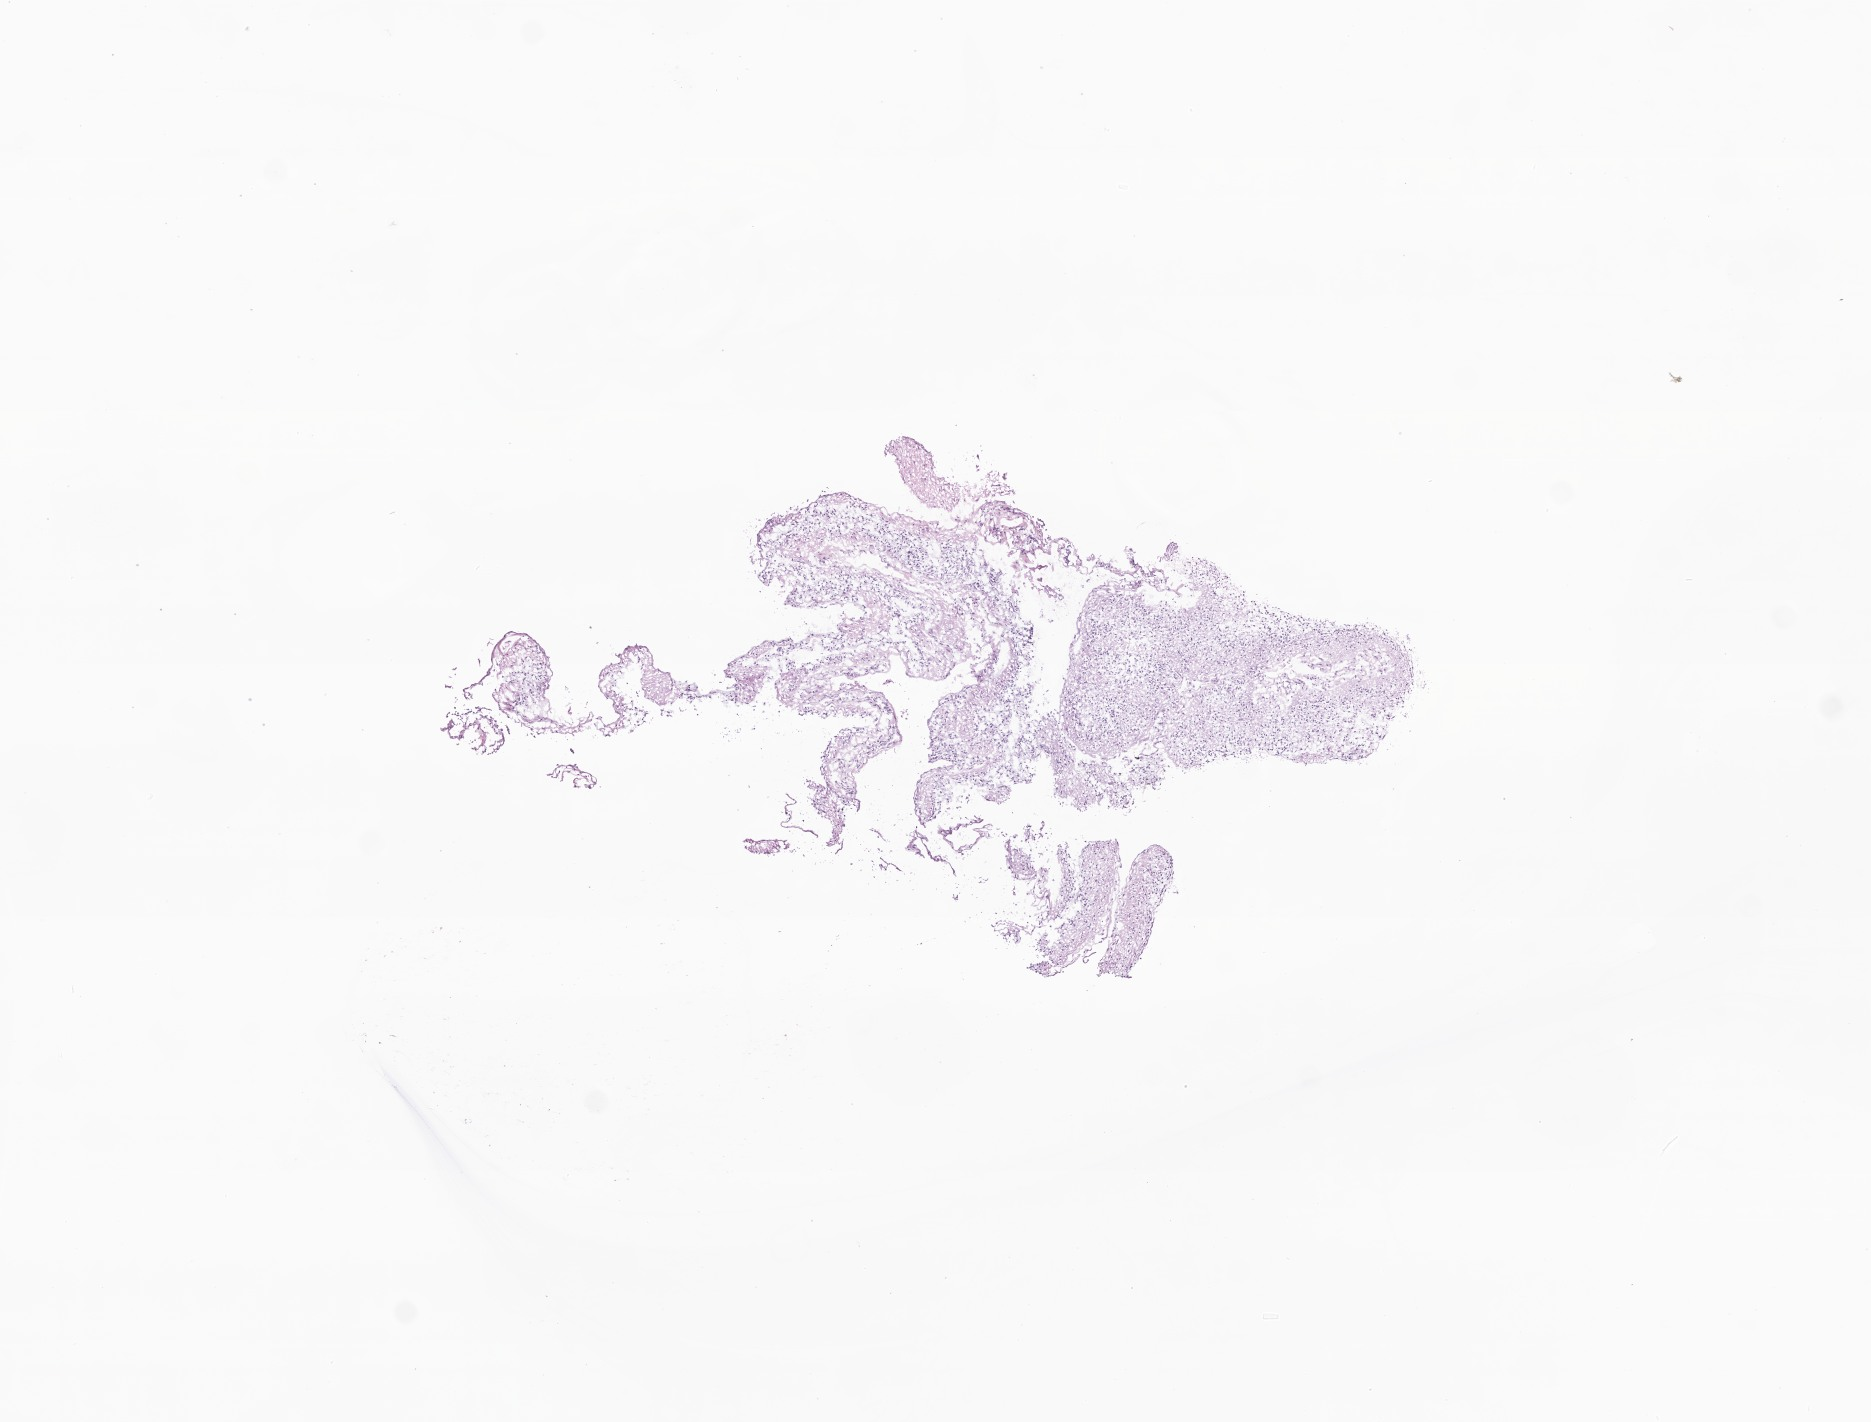
Hematoxylin and eosin (H&E) whole-slide image of tumor tissue from the cerebellum, whole scanned area (about 7.9 x 6.0 mm) shown as a low-resolution overview; frozen section (OCT-embedded). Patient male; age 40 months (3 years 4 months).
Recorded diagnosis: Pilocytic astrocytoma.